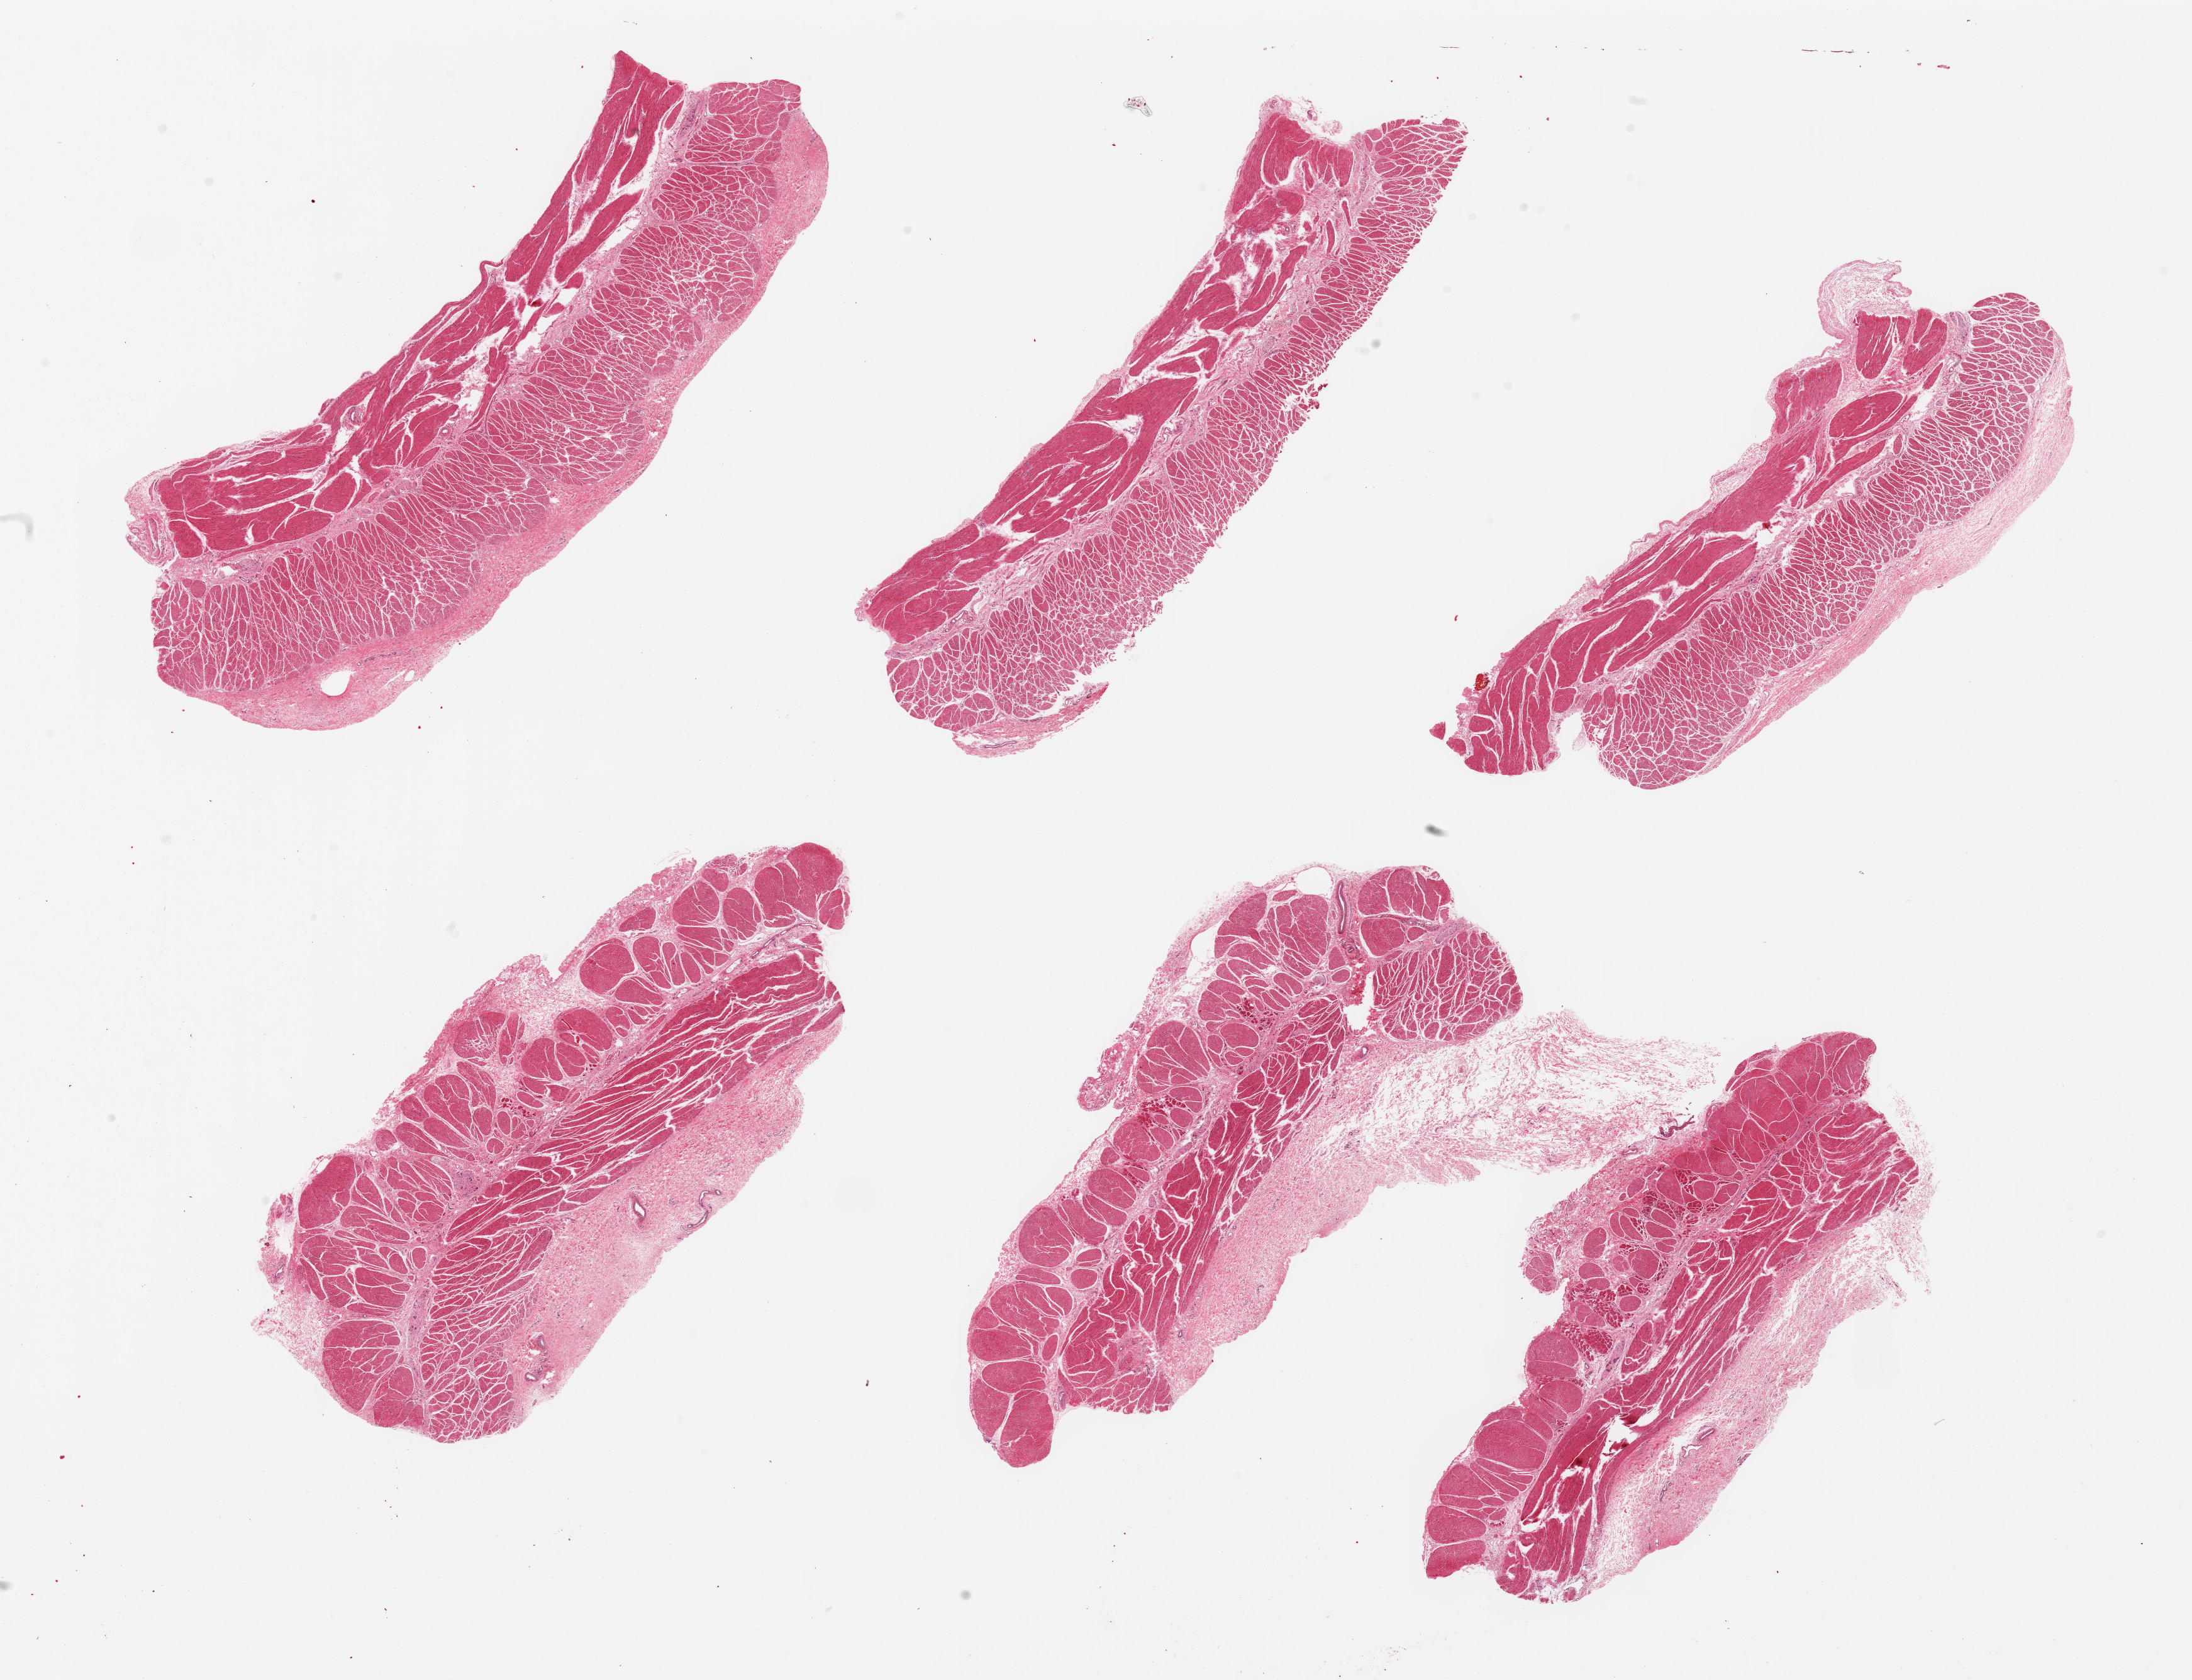
Whole-slide image, haematoxylin and eosin stain, brightfield, a low-resolution overview of the entire scanned area, about 27.6 x 21.1 mm (acquisition: 20x scan). PAXgene-fixed, paraffin-embedded tissue. Sampled site (target tissue): esophageal muscle. Tissue donor sample.
Pathologist's review note for this sample: 6 pieces all muscularis, focal attached serosal adipose tissues.